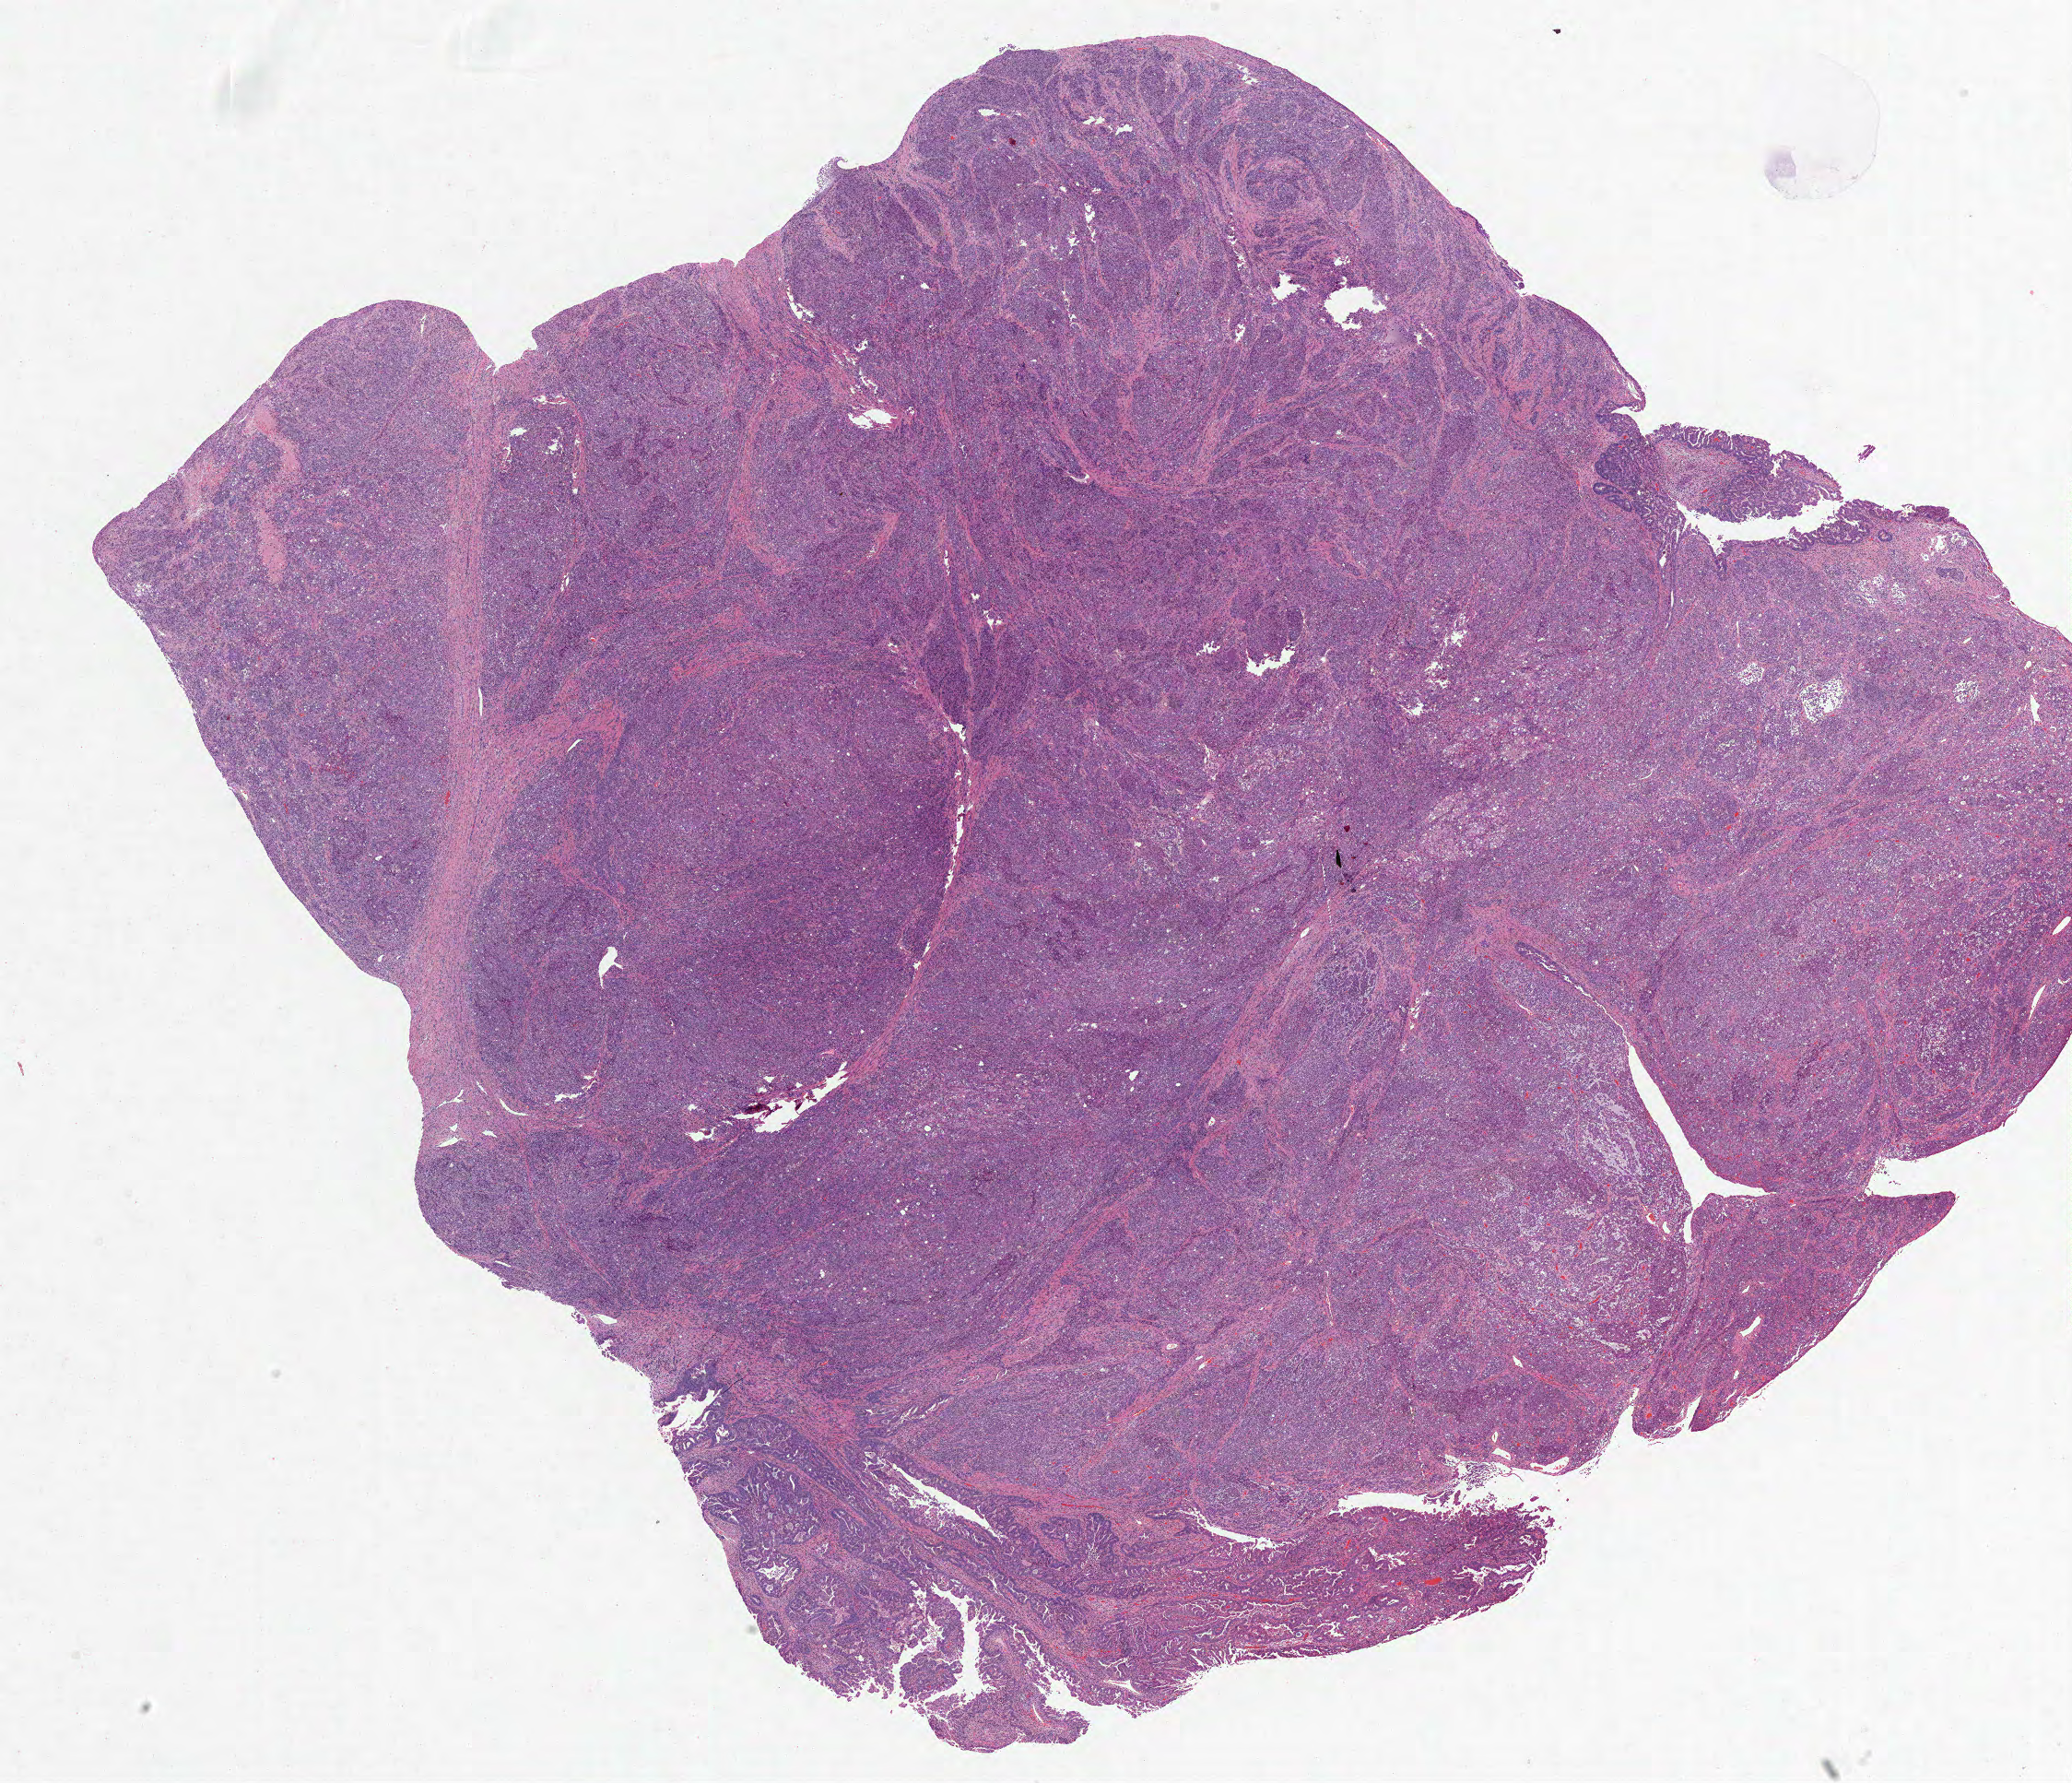
Digitized Hematoxylin and eosin (H&E) stained tissue section (whole slide) — a low-resolution overview of the entire scanned area, about 18.0 x 15.5 mm (from a 20x scan), formalin-fixed paraffin-embedded (FFPE) diagnostic section, uterus, primary tumour sample. Female patient; age at initial diagnosis 49 years. Histologic grade: G3 (poorly differentiated).
Diagnosis: Endometrioid adenocarcinoma, NOS (endometrium). FIGO stage: IVA.